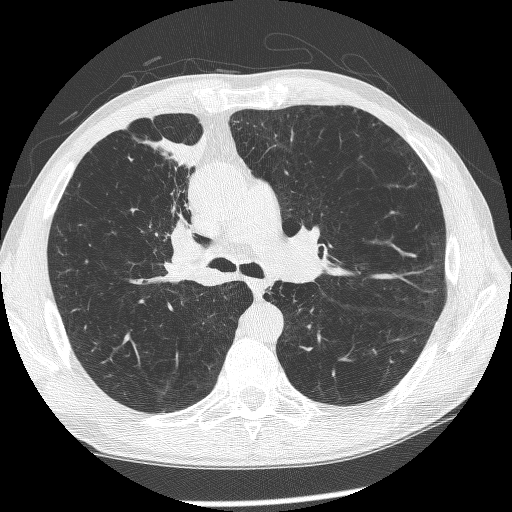
Axial slice from a low-dose chest CT screening exam, baseline screening round, lung window (W 1500 / L -600 HU), 120 kVp. Male participant, aged 60 years at enrolment. Current smoker at enrolment.
Lesion marked by an expert reader, bounding box <145,199,223,292> (left, top, right, bottom; pixels). The exam's reader record, not a measurement of the box and not confirmed to be the same lesion: non-calcified nodule or mass ≥4 mm, right upper lobe, 12 × 8 mm, spiculated (stellate) margins, mixed attenuation.